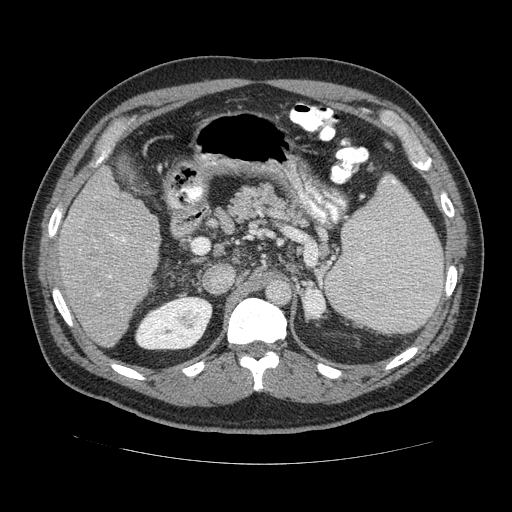
Contrast-enhanced abdominal CT (liver protocol), one axial slice; reconstruction kernel STANDARD; soft-tissue window (W 400 / L 40 HU); 2.5 mm slice thickness; 512 × 512 image matrix, field of view 400 × 400 mm. From the clinical record (not read from this slice): diagnosis: hepatocellular carcinoma (patient treated with transarterial chemoembolisation; whether this scan precedes or follows treatment is not stated here); TNM stage (as recorded): Stage-II; Child-Pugh class: B; tumour nodularity: multinodular.
Annotated regions visible in this slice (semi-automatic segmentation, software-assisted and operator-edited):
- liver parenchyma outside the tumour (the mass and vessels are separate outlines, so this box may not span the whole liver): bounding box (x1, y1, x2, y2) in pixels: (48, 164, 160, 348)
- liver vessels: (97, 236, 129, 295)